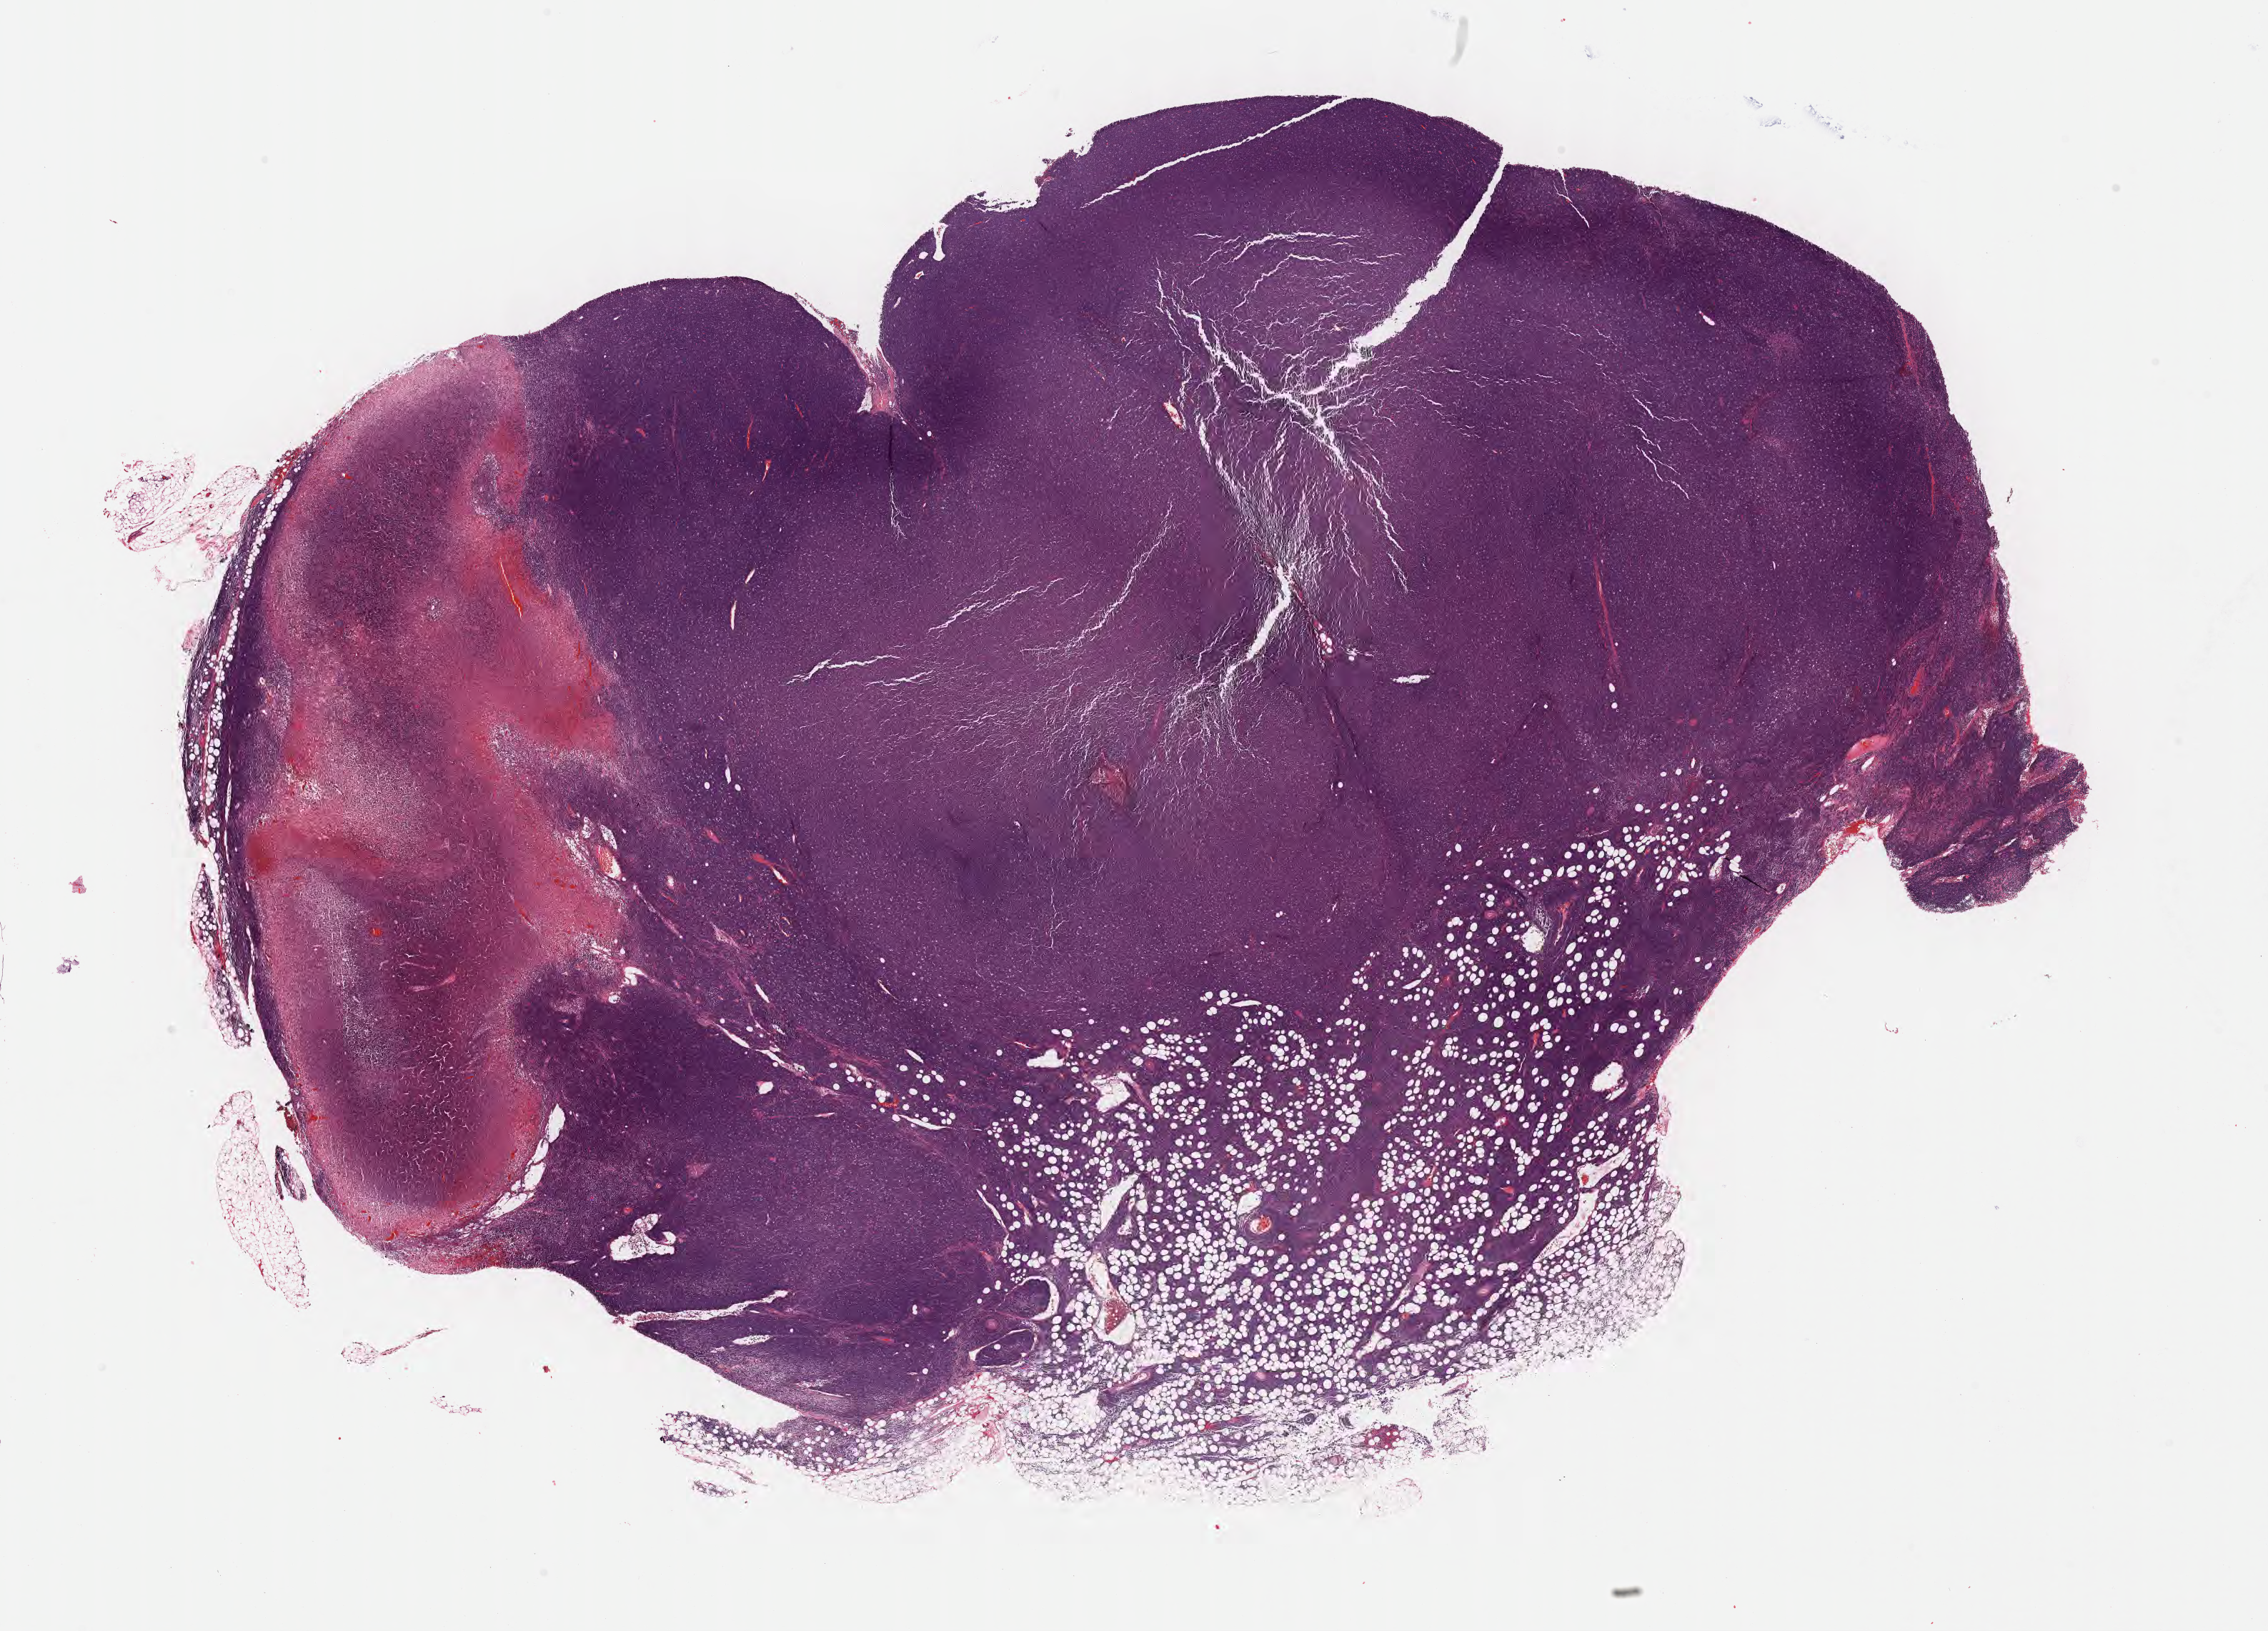
Hematoxylin and eosin (H&E) whole-slide image — shown as a low-resolution overview of the whole scanned area (about 25.7 x 18.5 mm). Formalin-fixed, paraffin-embedded (FFPE) tissue. Primary tumor. Patient male; 57 years old. Pathologist review of this section (percent, as recorded): tumor cells 70%, tumor nuclei 90%, stromal cells 10%, necrosis 20%, normal cells 0%. Infiltration values recorded for this section: lymphocyte infiltration 80%, monocyte infiltration 10%, neutrophil infiltration 5%.
* Ann Arbor stage (patient): Stage IV
* section: bottom of the tissue portion
* diagnosis: Burkitt lymphoma, NOS